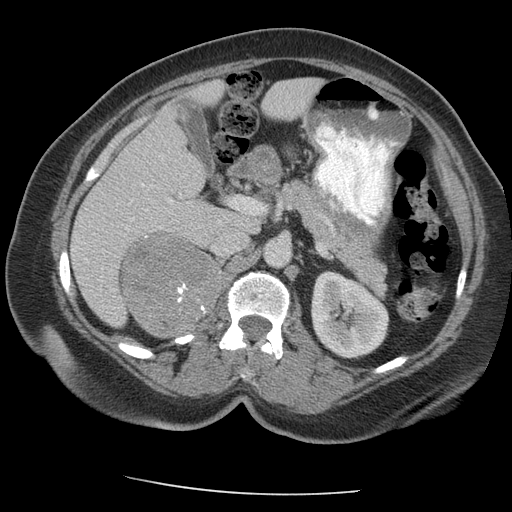
Contrast-enhanced abdominal CT, one axial slice. Position 121 of 163 along the scan axis. Reconstruction kernel STANDARD. Intravenous contrast given. Soft-tissue window (W 400 / L 40 HU). 2.5 mm slice thickness. 512 × 512 image matrix, field of view 360 × 360 mm. Patient: female, 70 years. Case-level facts recorded for this patient, not image findings: diagnosis: adrenocortical carcinoma; tumour side: right adrenal; tumour size at pathology: 9.5 cm; Ki-67 index: 5 %; stage (as recorded): 2.
Annotated regions visible in this slice (semi-automatic segmentation, software-assisted and operator-edited):
- mass: box from (x=124, y=237) to (x=222, y=336) px